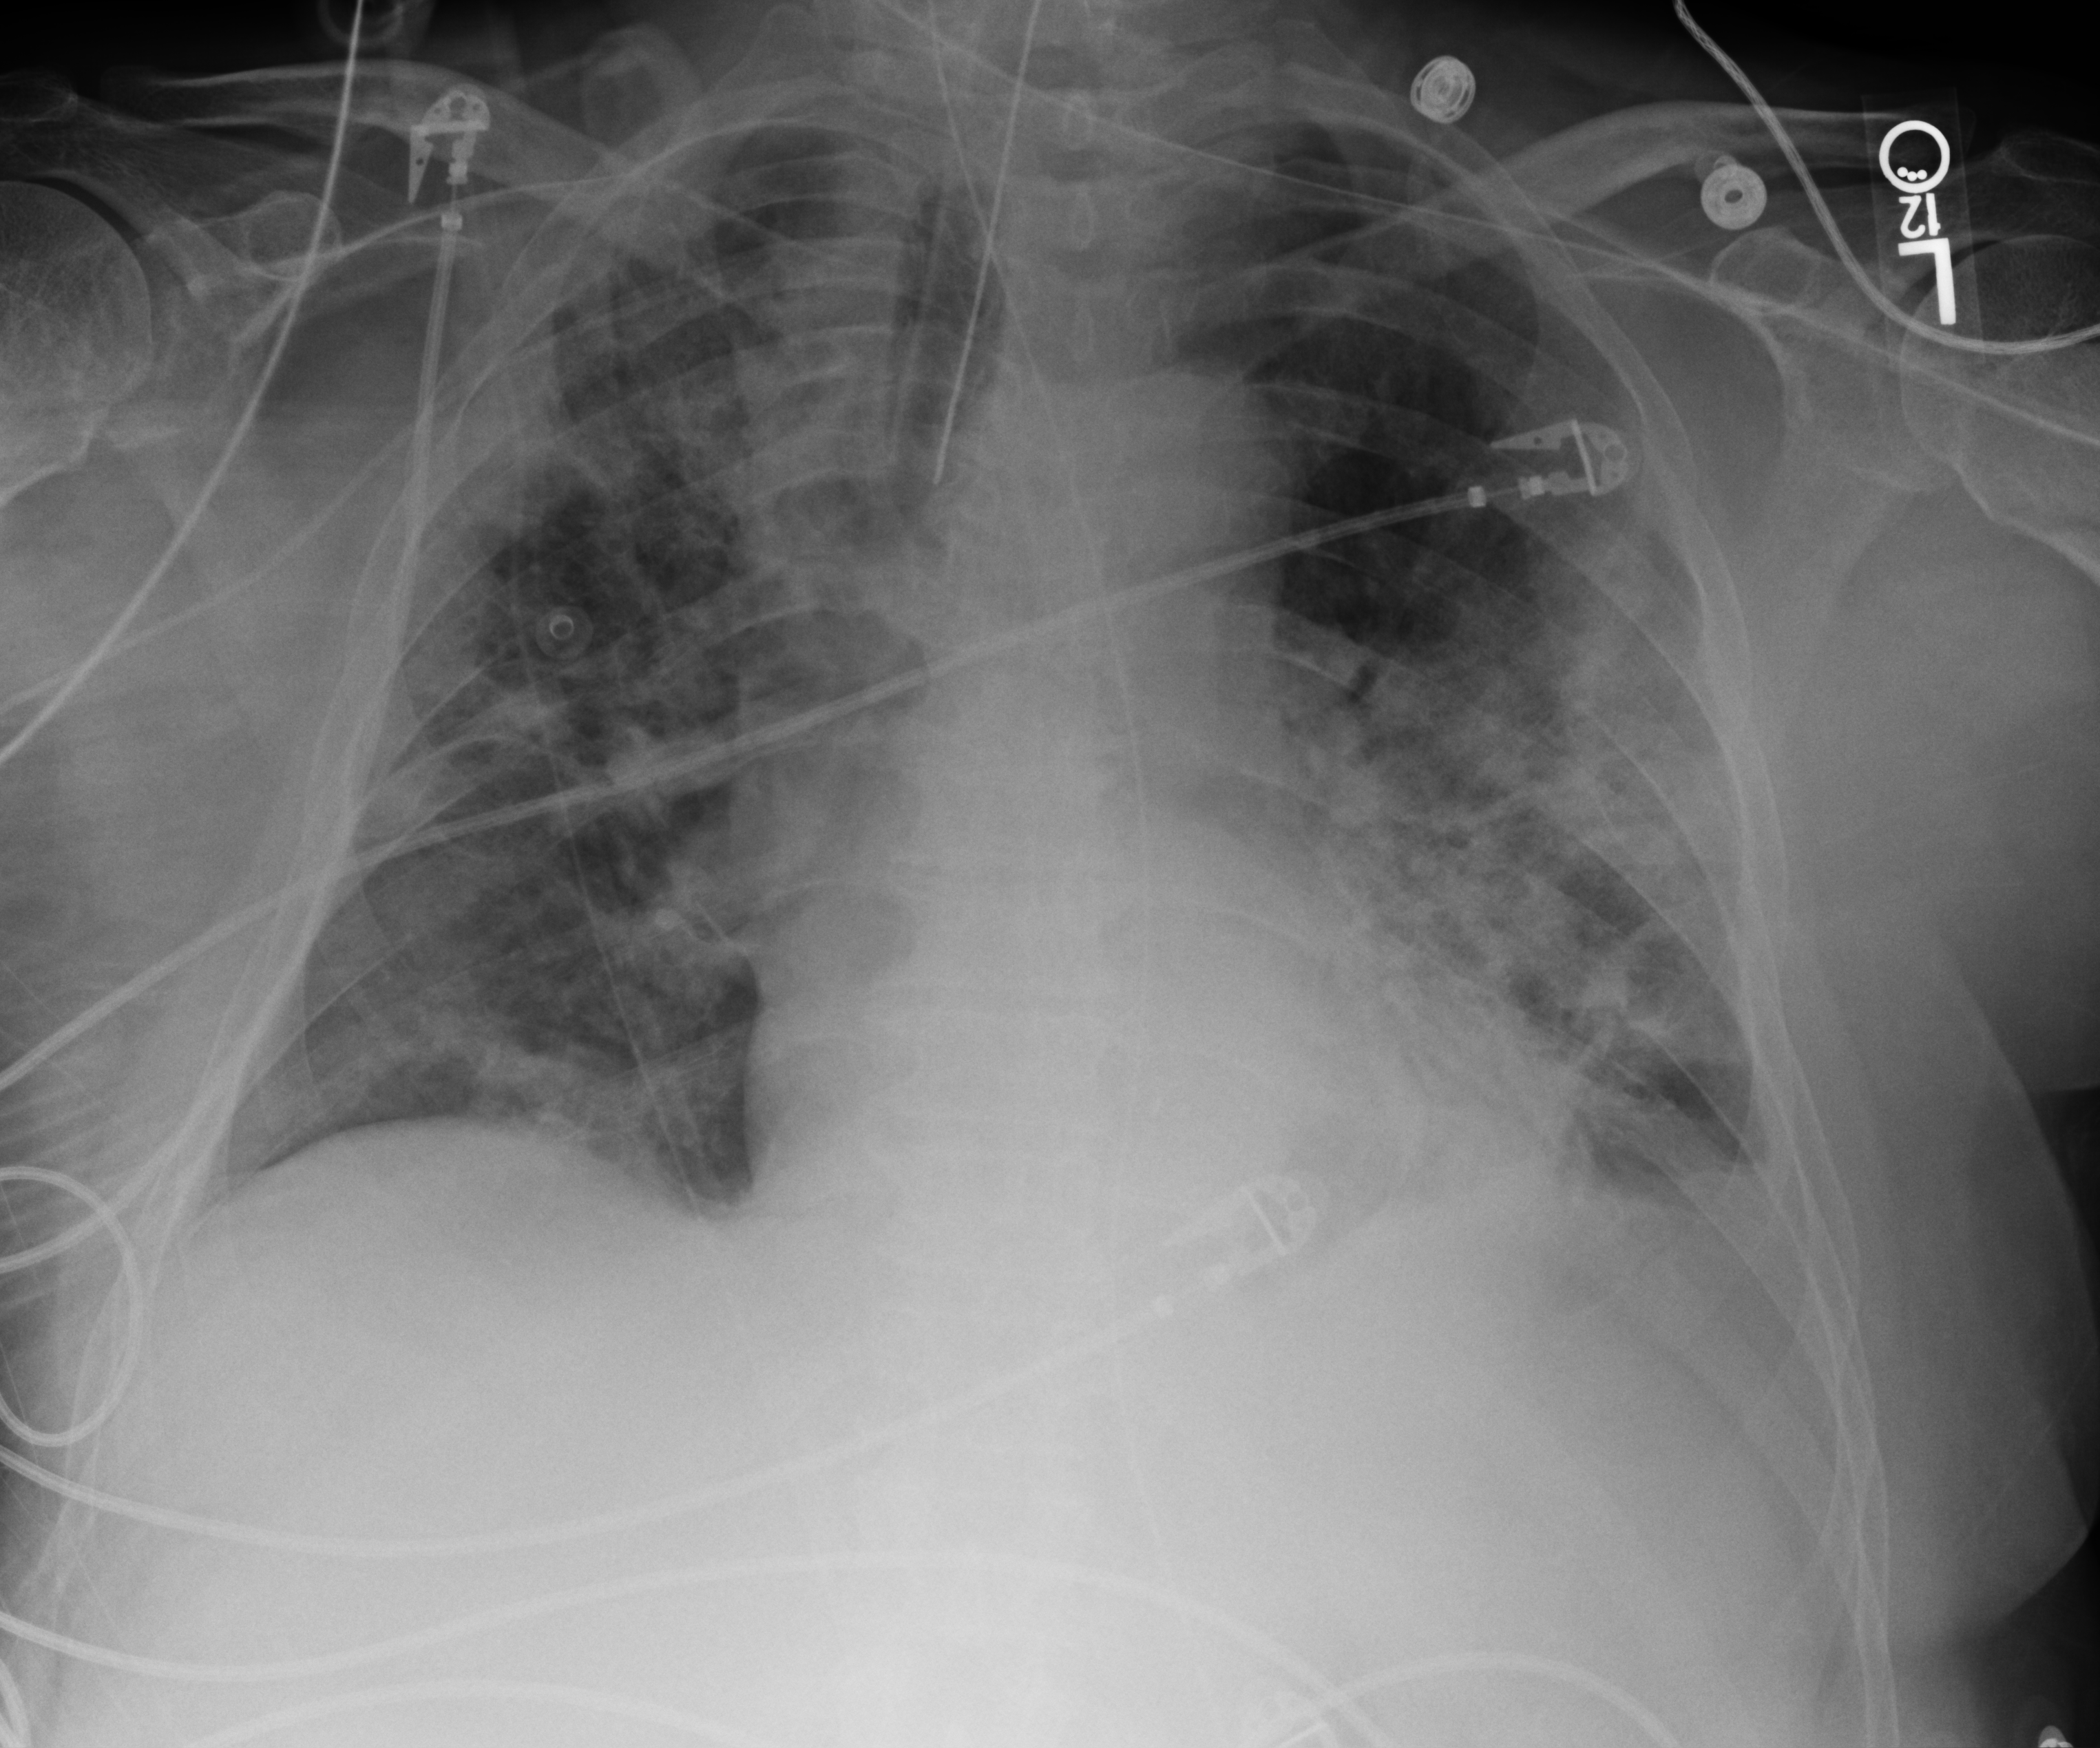
Portable chest radiograph; anteroposterior (AP) projection. Patient hospitalised with COVID-19; male, aged 60–74 years.
Admission-level facts for this patient (not findings on this image; timing relative to this image not recorded):
- admitted to intensive care during this hospital stay: yes
- mechanically ventilated during this hospital stay: yes